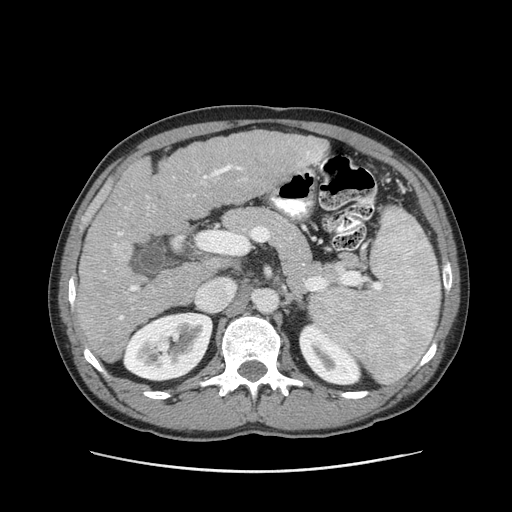
Contrast-enhanced abdominal CT (liver protocol), one axial slice. Slice 50 of 93 in the series (ordered by position). Reconstruction kernel STANDARD. Soft-tissue window (W 400 / L 40 HU). 2.5 mm slice thickness. 512 × 512 image matrix. Case-level facts recorded for this patient, not image findings: diagnosis: hepatocellular carcinoma (patient treated with transarterial chemoembolisation; whether this scan precedes or follows treatment is not stated here); TNM stage (as recorded): Stage-II; Child-Pugh class: A; tumour differentiation: moderately differentiated; tumour size: 1 cm.
Annotated regions visible in this slice (semi-automatic segmentation, software-assisted and operator-edited):
- liver parenchyma outside the tumour (the mass and vessels are separate outlines, so this box may not span the whole liver): bounding box (x1, y1, x2, y2) in pixels: (76, 130, 328, 362)
- liver vessels: (104, 150, 323, 320)